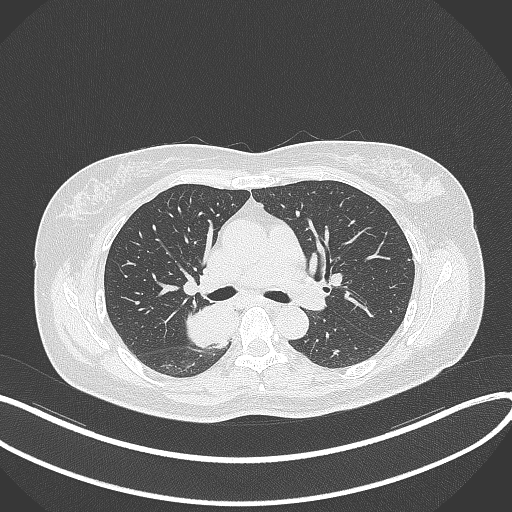
Chest CT, one axial slice. Position 225 of 331 along the scan axis. Reconstruction kernel B70f. 120 kVp. Lung window (W 1500 / L -600 HU). 1 mm slice thickness. 512 × 512 image matrix. Female patient, age 54 years. Case-level facts recorded for this patient, not image findings: clinical TNM (as recorded): T4 N0 M0.
Annotated regions visible in this slice (bounding box drawn by a radiologist):
- lung tumour (recorded histology: adenocarcinoma): bounding box <181,296,242,351> (left, top, right, bottom; pixels)